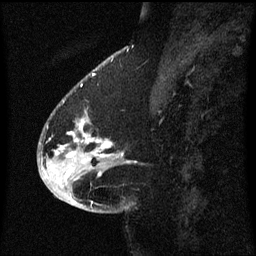
Breast MRI (dynamic contrast-enhanced), one sagittal slice. Slice 23 of 60 in the series (ordered by position). Dynamic contrast-enhanced series, image 2 of 3 at this slice position (ordered by acquisition). 1.5 T. TE 4.2 ms, TR 8.4 ms. 256 × 256 image matrix, field of view 200 × 200 mm. Female patient, age 54 years. From the clinical record (not read from this slice): setting: breast cancer imaged before/during neoadjuvant chemotherapy; receptor status: HR-positive, HER2-negative.
Outlined on this slice (semi-automatic segmentation, software-assisted and operator-edited):
- analysis volume of interest (the breast-tissue region the enhancement analysis was run in; not a lesion): bounding box [x1, y1, x2, y2] px = [46, 100, 123, 171]
- tumour enhancement mask (voxels above the 70 % enhancement threshold inside the analysis volume of interest): [69, 120, 113, 157]